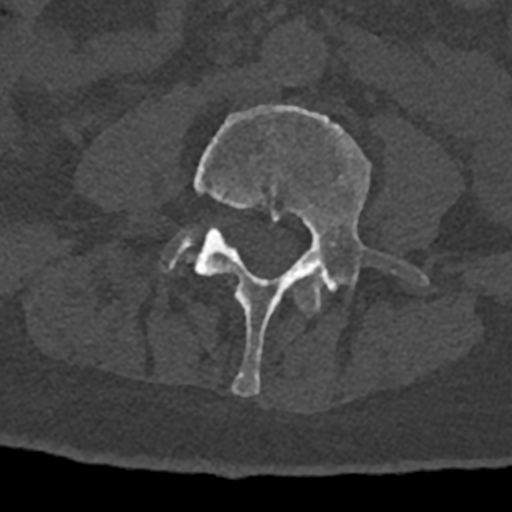
CT including the spine, one axial slice. Position 260 of 797 along the scan axis. Reconstruction kernel Br40s/3. 120 kVp. Bone window (W 1800 / L 400 HU). 0.5 mm slice thickness. 512 × 512 image matrix. Patient: male, 74 years. Case-level facts recorded for this patient, not image findings: primary cancer: renal.
Structures marked on this image (semi-automatically segmented with operator editing):
- L3 vertebra: bounding box [x1, y1, x2, y2] px = [294, 274, 323, 314]
- L4 vertebra: [192, 105, 429, 397]
- L5 vertebra: [164, 231, 192, 268]